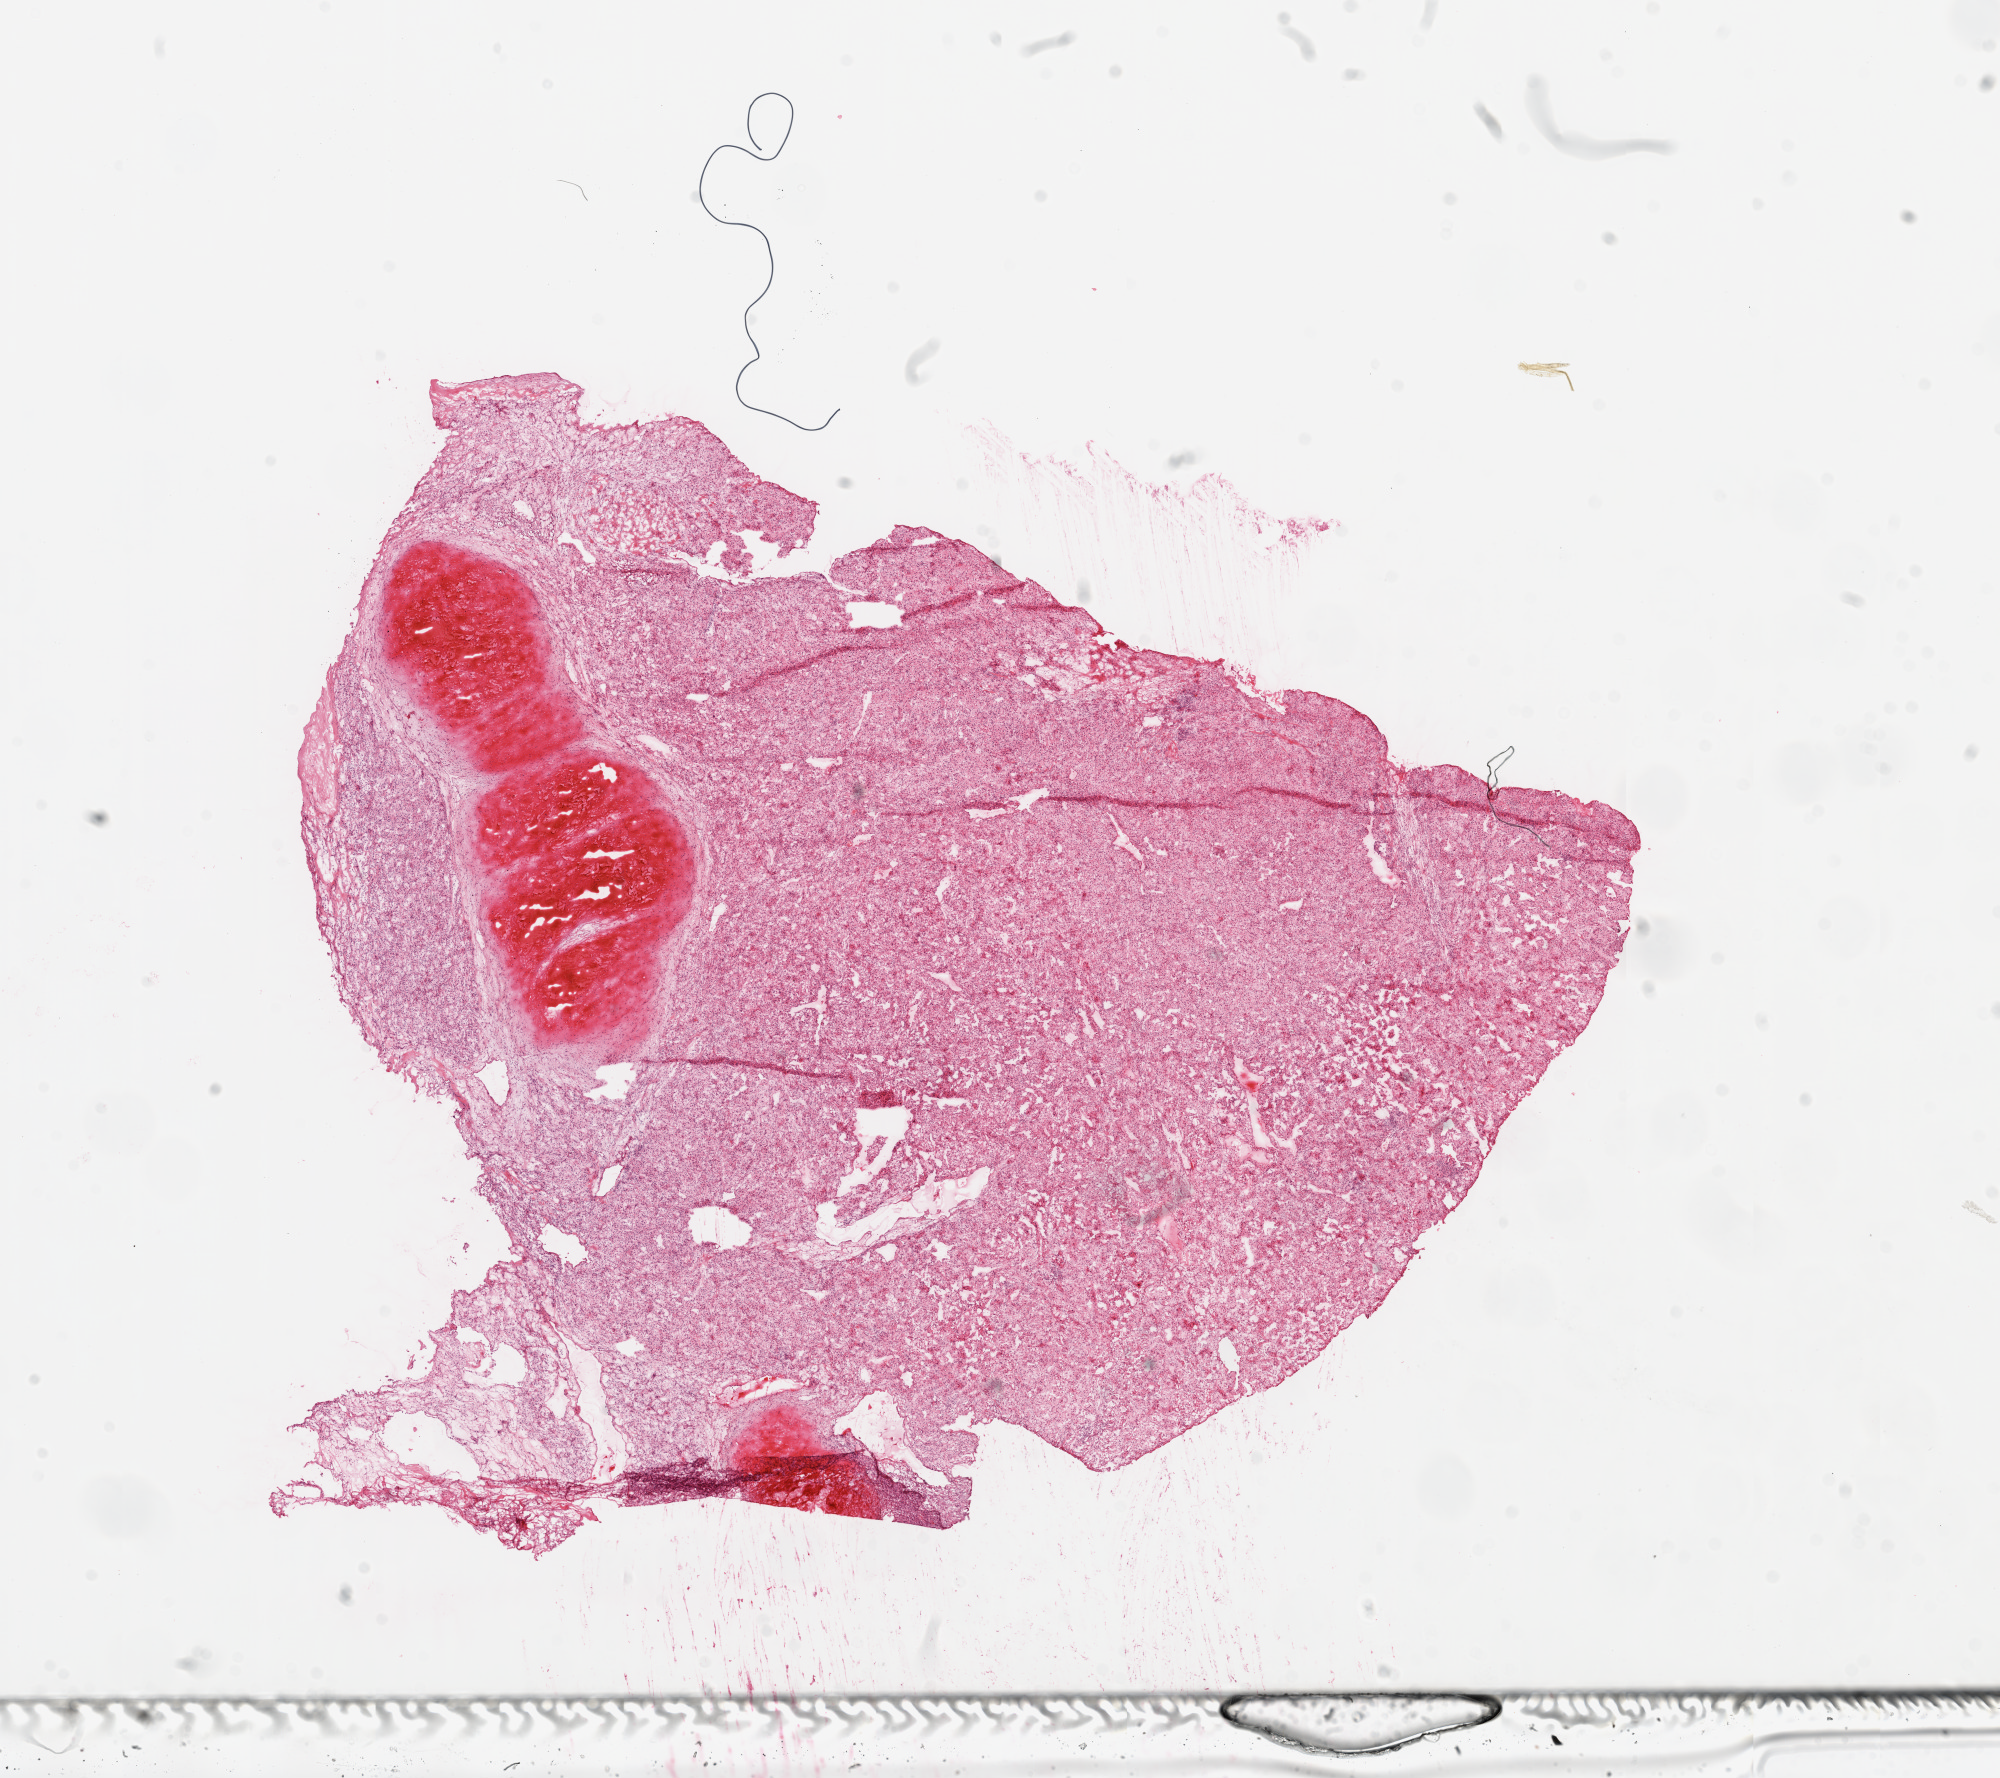
Whole-slide histology image, H&E, whole scanned area (about 16.0 x 14.3 mm, acquisition: 20x scan) shown as a low-resolution overview, frozen section from the top of the tissue portion, primary tumour sample from the kidney. Male patient; age at initial diagnosis 52 years. Histologic grade: G4 (undifferentiated). Pathologist review of this section (percent, as recorded): tumour cells 90%, tumour nuclei 90%, normal cells 0%, stromal cells 10%, necrosis 0%.
AJCC pathologic stage: IV. Histologic diagnosis: Clear cell adenocarcinoma, NOS. Laterality: right.